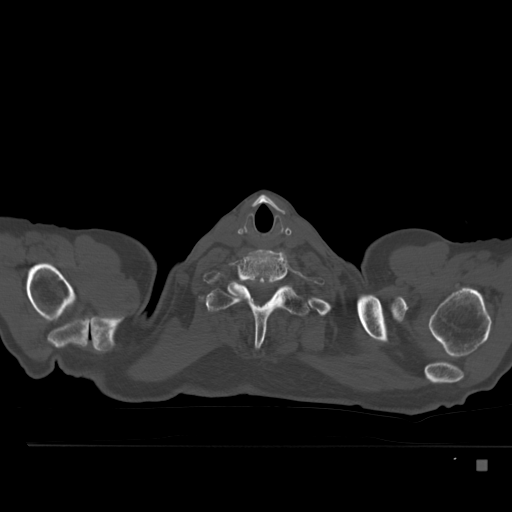
CT including the spine, one axial slice; slice 432 of 517 in the series (ordered by position); 120 kVp; bone window (W 1800 / L 400 HU); 512 × 512 image matrix, field of view 408 × 408 mm. Male patient, age 70 years. Case-level facts recorded for this patient, not image findings: primary cancer: renal; vertebrae with lytic lesions (as recorded): T4, T6, T10, T12, L3, L4, L5.
Outlined on this slice (semi-automatic segmentation, software-assisted and operator-edited):
- T1 vertebra: bounding box (x1, y1, x2, y2) in pixels: (202, 281, 310, 347)